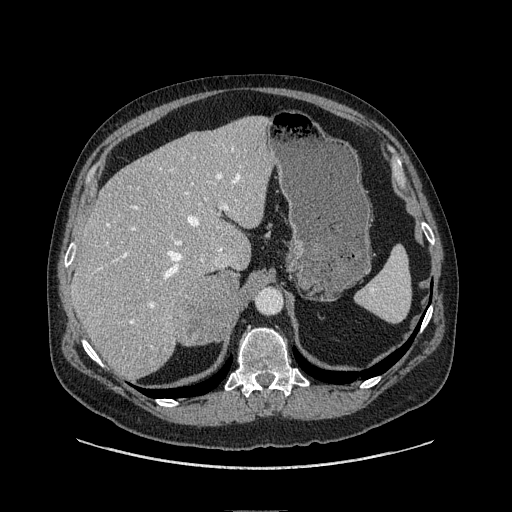
Contrast-enhanced abdominal CT, one axial slice. Position 74 of 149 along the scan axis. Soft-tissue window (W 400 / L 40 HU). 1.25 mm slice thickness. 512 × 512 image matrix, field of view 440 × 440 mm. Male patient. From the clinical record (not read from this slice): diagnosis: adrenocortical carcinoma; tumour side: right adrenal; tumour size at pathology: 7.5 cm.
Outlined on this slice (semi-automatically segmented with operator editing):
- mass: box from (x=175, y=272) to (x=241, y=345) px